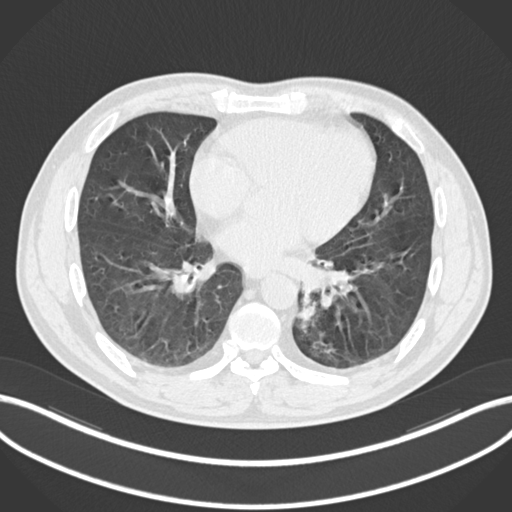
Chest CT, one axial slice. Slice 88 of 223 in the series (ordered by position). 120 kVp. Lung window (W 1500 / L -600 HU). 1 mm slice thickness. 512 × 512 image matrix, field of view 400 × 400 mm. Patient: male, 50 years. From the clinical record (not read from this slice): clinical TNM (as recorded): T2a N3 M0.
Outlined on this slice (bounding box drawn by a radiologist):
- lung tumour (recorded histology: squamous cell carcinoma): bounding box <298,289,325,333> (left, top, right, bottom; pixels)